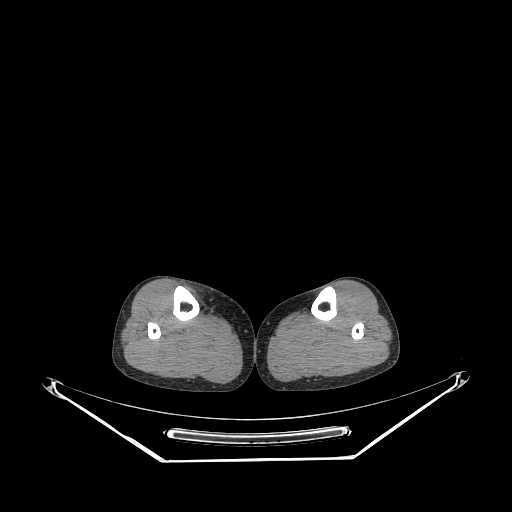
CT of an extremity soft-tissue mass (from a PET/CT study), one axial slice. Position 129 of 267 along the scan axis. Reconstruction kernel STANDARD. Soft-tissue window (W 400 / L 40 HU). 3.75 mm slice thickness. 512 × 512 image matrix. Female patient. From the clinical record (not read from this slice): histological type: undifferentiated – high grade; grade: high; site of the primary tumour: right thigh.
Structures marked on this image (expert contour drawn on MRI and transferred to this co-registered scan by the dataset authors):
- gross tumour volume (mass): bounding box [x1, y1, x2, y2] px = [192, 295, 195, 298]